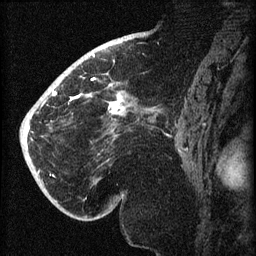
Breast MRI (dynamic contrast-enhanced), one sagittal slice. Dynamic contrast-enhanced series, image 2 of 3 at this slice position (ordered by acquisition). 1.5 T. TE 4.2 ms, TR 8.2 ms. 2 mm slice thickness. 256 × 256 image matrix. Female patient, age 71 years.
Outlined on this slice (semi-automatic segmentation, software-assisted and operator-edited):
- analysis volume of interest (the breast-tissue region the enhancement analysis was run in; not a lesion): bounding box <40,72,148,196> (left, top, right, bottom; pixels)
- tumour enhancement mask (voxels above the 70 % enhancement threshold inside the analysis volume of interest): <43,77,123,114>